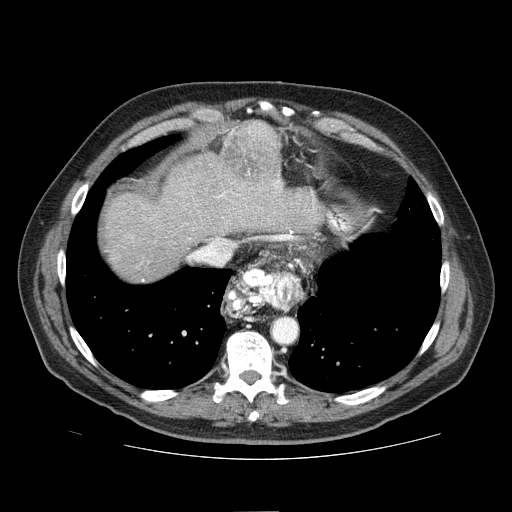
Contrast-enhanced abdominal CT (liver protocol), one axial slice. Position 65 of 81 along the scan axis. 100 kVp. One of 2 acquisitions stored at this slice position. Soft-tissue window (W 400 / L 40 HU). 2.5 mm slice thickness. 512 × 512 image matrix, field of view 400 × 400 mm. From the clinical record (not read from this slice): diagnosis: hepatocellular carcinoma (patient treated with transarterial chemoembolisation; whether this scan precedes or follows treatment is not stated here); TNM stage (as recorded): Stage-IIIA; Child-Pugh class: A; tumour differentiation: well differentiated; tumour nodularity: multinodular.
Outlined on this slice (semi-automatic segmentation, software-assisted and operator-edited):
- liver parenchyma outside the tumour (the mass and vessels are separate outlines, so this box may not span the whole liver): box from (x=104, y=152) to (x=322, y=282) px
- mass: (x=219, y=120)–(x=282, y=191)
- liver vessels: (x=143, y=180)–(x=315, y=281)